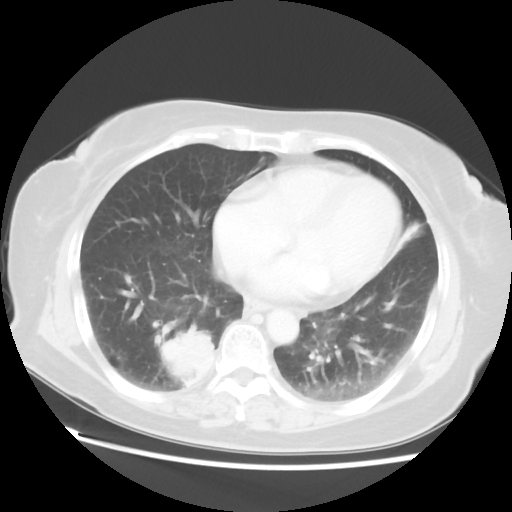
Chest CT, one axial slice; slice 22 of 52 in the series (ordered by position); 120 kVp; lung window (W 1500 / L -600 HU); 5 mm slice thickness; 512 × 512 image matrix, field of view 356 × 356 mm. Patient: female, 69 years. Case-level facts recorded for this patient, not image findings: clinical TNM (as recorded): T2 N1 M1a.
Annotated regions visible in this slice (bounding box drawn by a radiologist):
- lung tumour (recorded histology: adenocarcinoma): bounding box (x1, y1, x2, y2) in pixels: (153, 324, 221, 389)